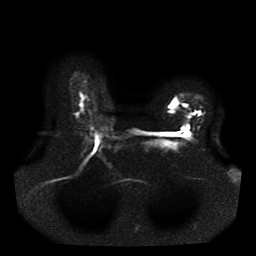
Breast MRI, one axial slice. Position 30 of 41 along the scan axis. Diffusion-weighted series; image 2 of 4 stored at this slice position (different b-values; order by instance number). 1.5 T. 5 mm slice thickness. 256 × 256 image matrix, field of view 330 × 330 mm. Female patient.
Structures marked on this image (expert manual segmentation):
- tumour on diffusion-weighted imaging: bounding box (x1, y1, x2, y2) in pixels: (171, 101, 176, 107)